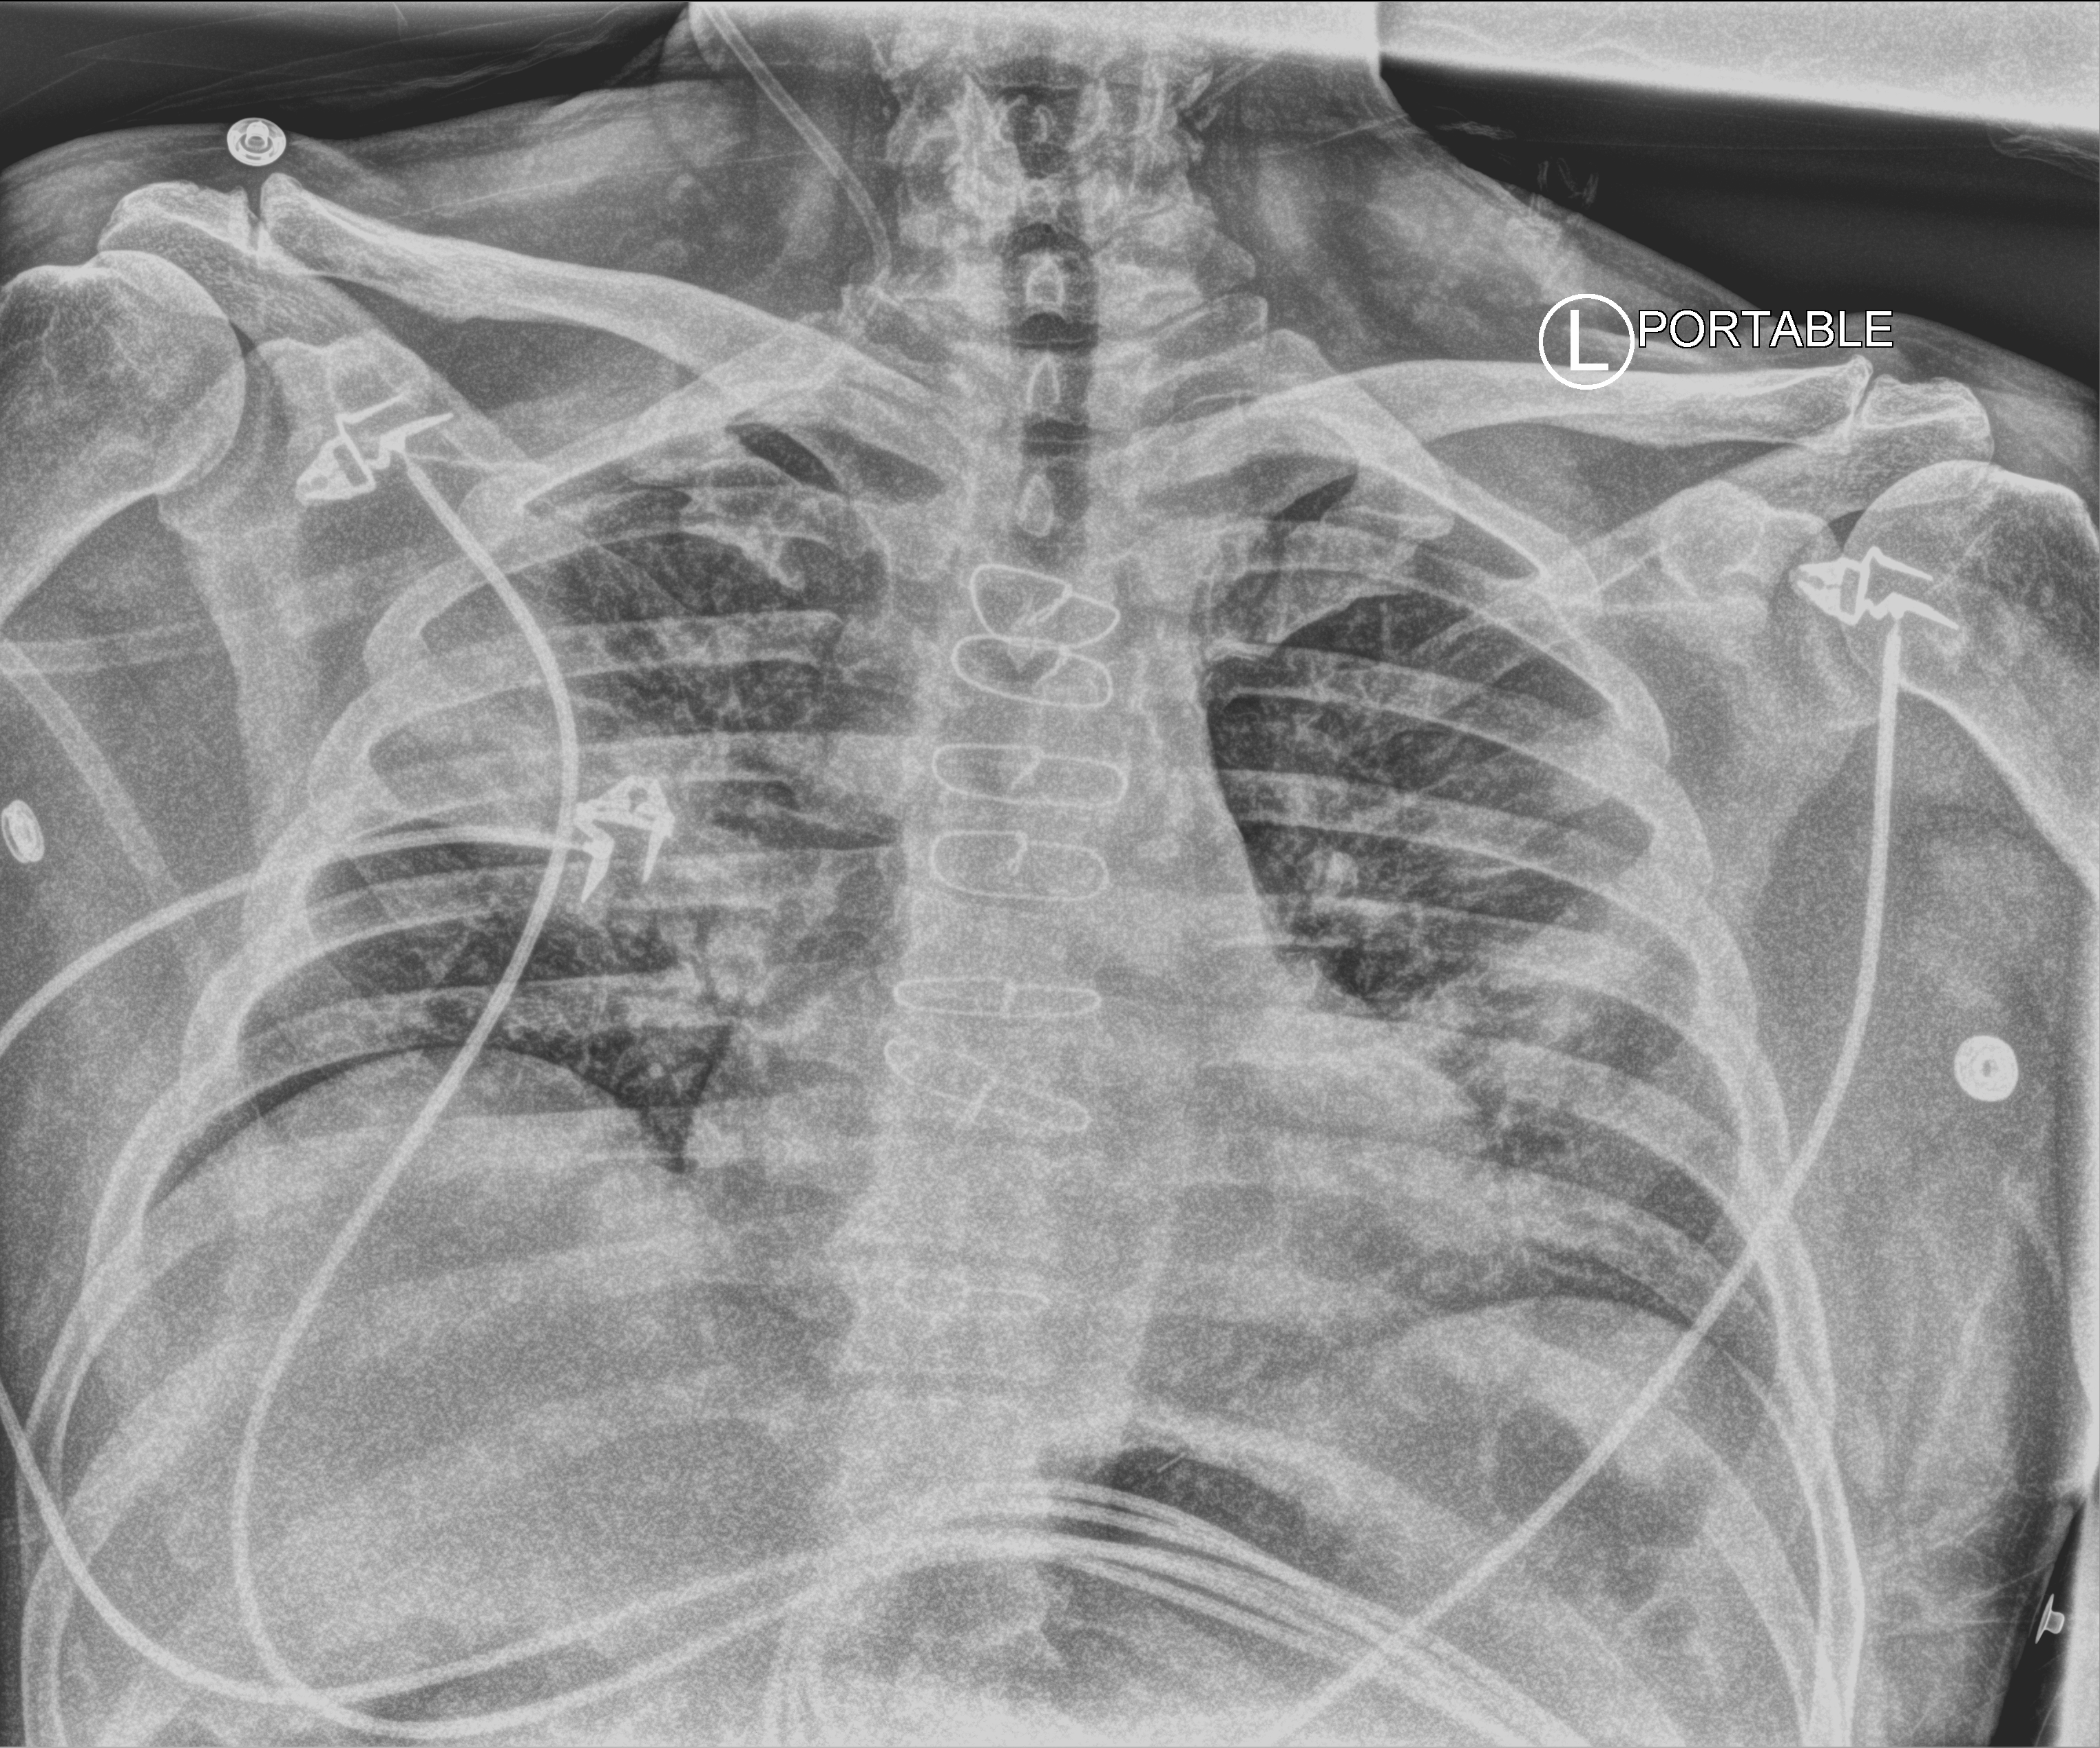
Chest X-ray (portable), anteroposterior (AP) projection. Patient hospitalised with COVID-19; male, aged 60–74 years.
From the hospital-stay record, not from the radiograph (when in the stay this image was taken is not recorded):
- length of hospital stay: 44 days
- mechanically ventilated during this hospital stay: yes